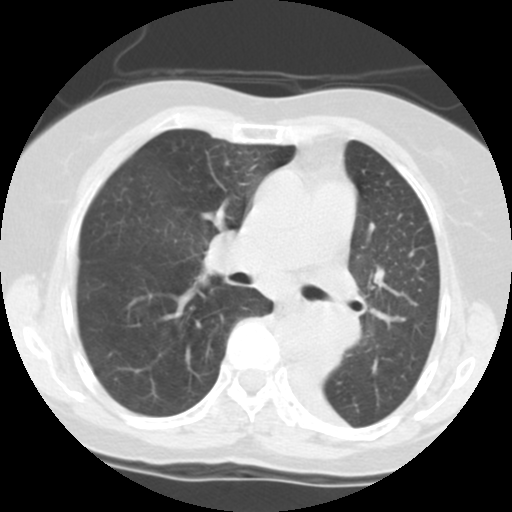
Low-dose screening chest CT, one axial slice. Position 72 of 113 along the scan axis. Reconstruction kernel STANDARD. 140 kVp. Lung window (W 1500 / L -600 HU). 2.5 mm slice thickness. 512 × 512 image matrix, field of view 280 × 280 mm.
Annotated regions visible in this slice (manually delineated by an expert):
- lesion 1 (tumor, left main bronchus): bounding box [x1, y1, x2, y2] px = [306, 302, 360, 354]